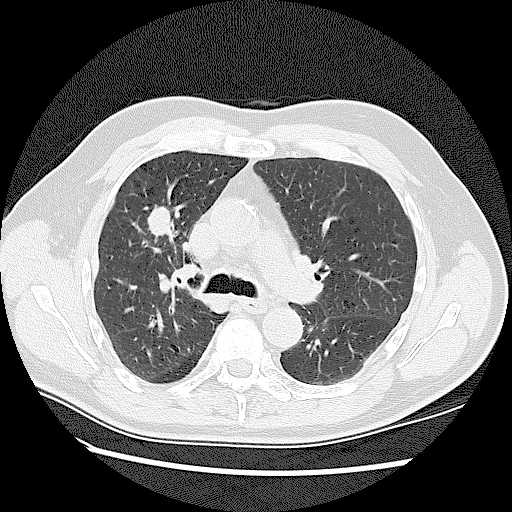
Low-dose screening chest CT, one axial slice. Reconstruction kernel LUNG. 120 kVp. Lung window (W 1500 / L -600 HU). 512 × 512 image matrix, field of view 360 × 360 mm.
Outlined on this slice (manually delineated by an expert):
- lesion 1 (tumor, upper lobe of right lung): bounding box [x1, y1, x2, y2] px = [147, 207, 171, 238]